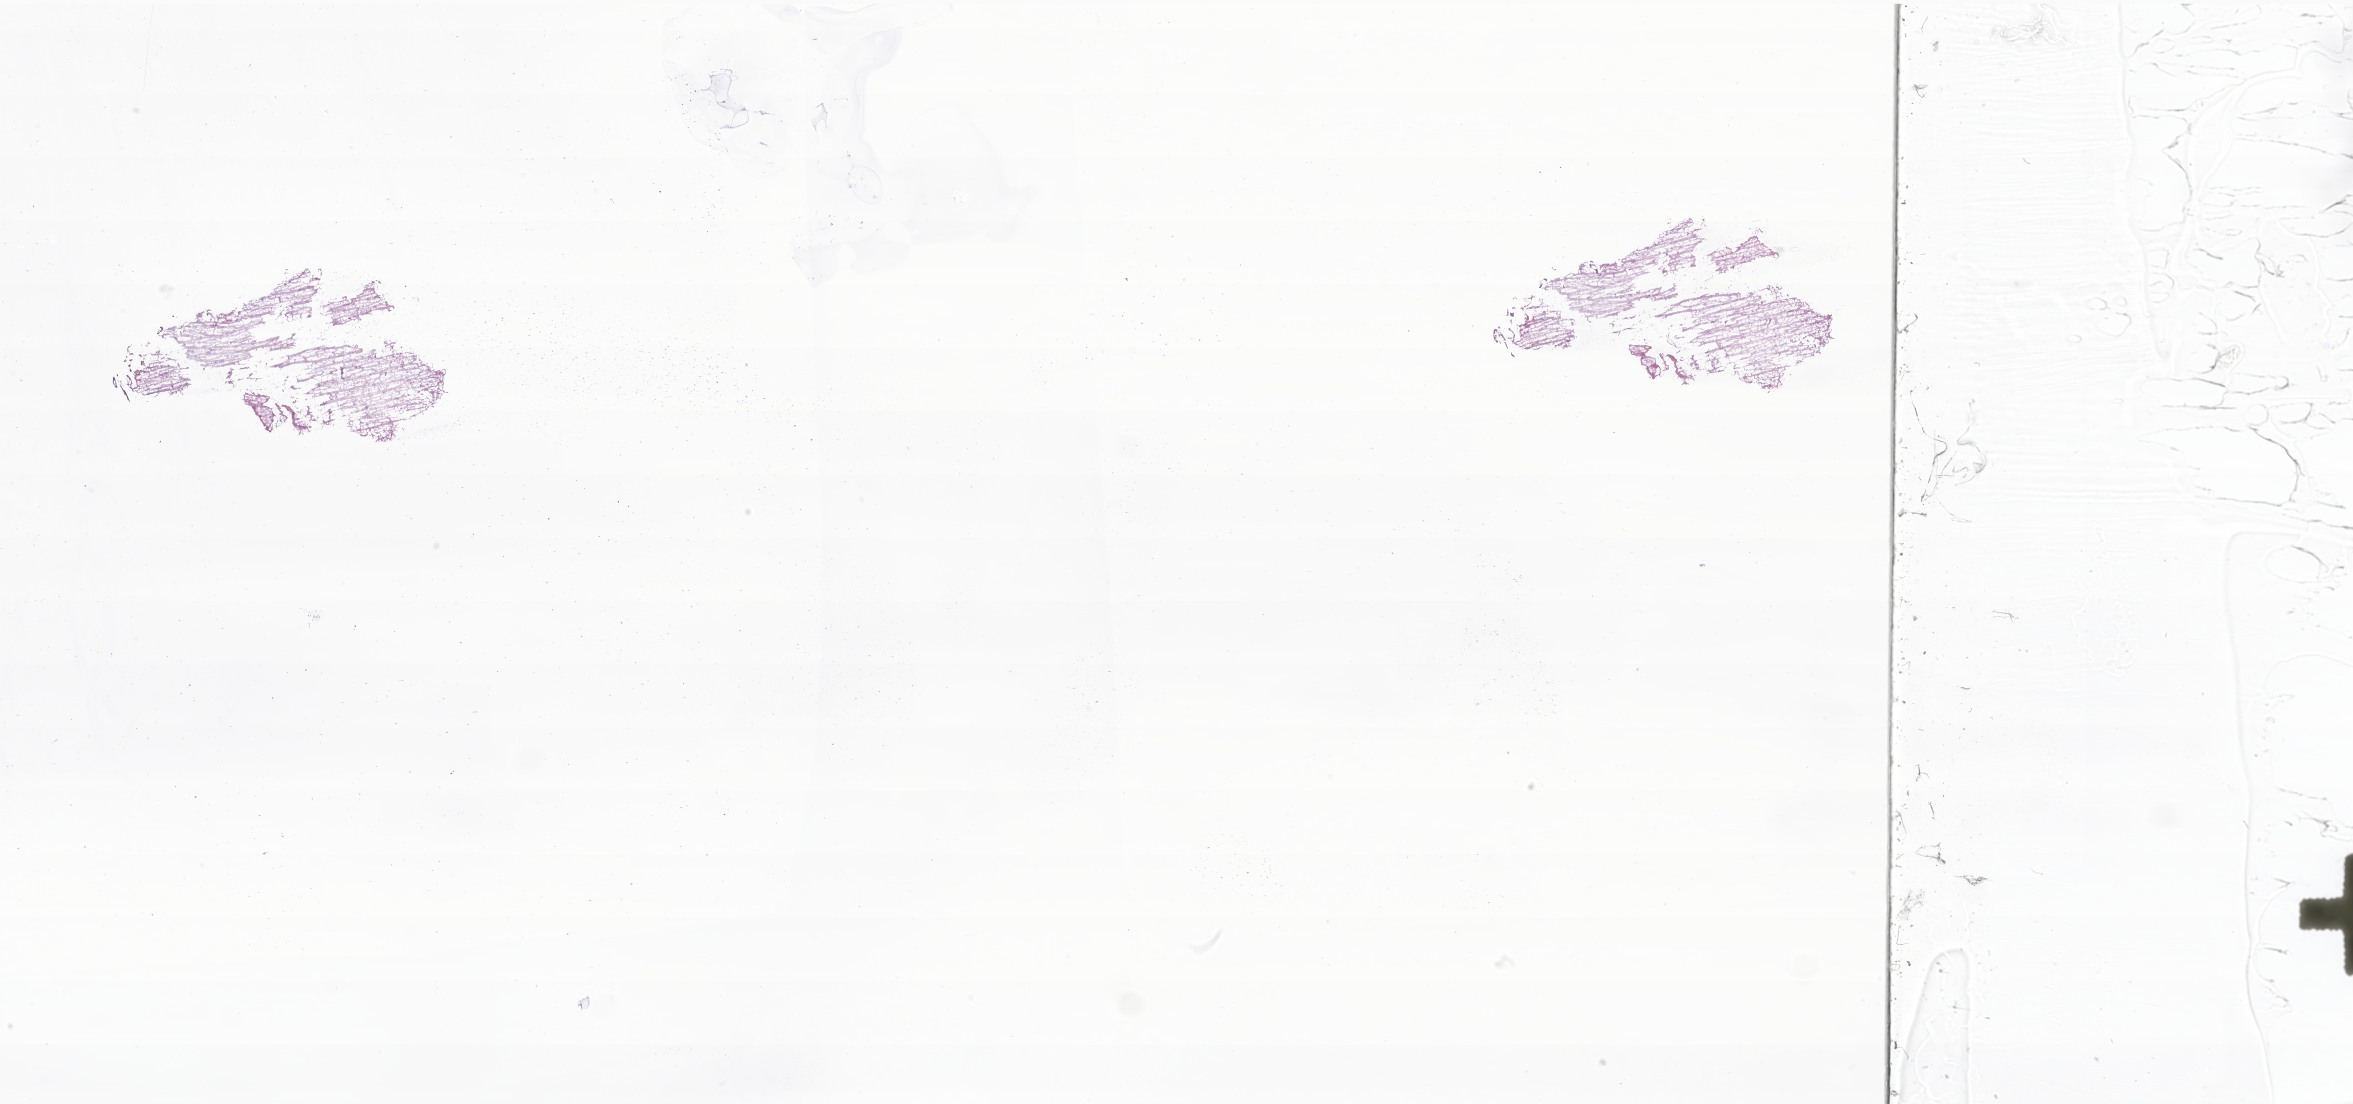
Digitized haematoxylin and eosin-stained section of tumor tissue from the brain — whole scanned area (about 39.7 x 18.6 mm) shown as a low-resolution overview, frozen section (OCT-embedded). Male patient, age 159 months (13 years 3 months).
* recorded diagnosis: Pilocytic astrocytoma